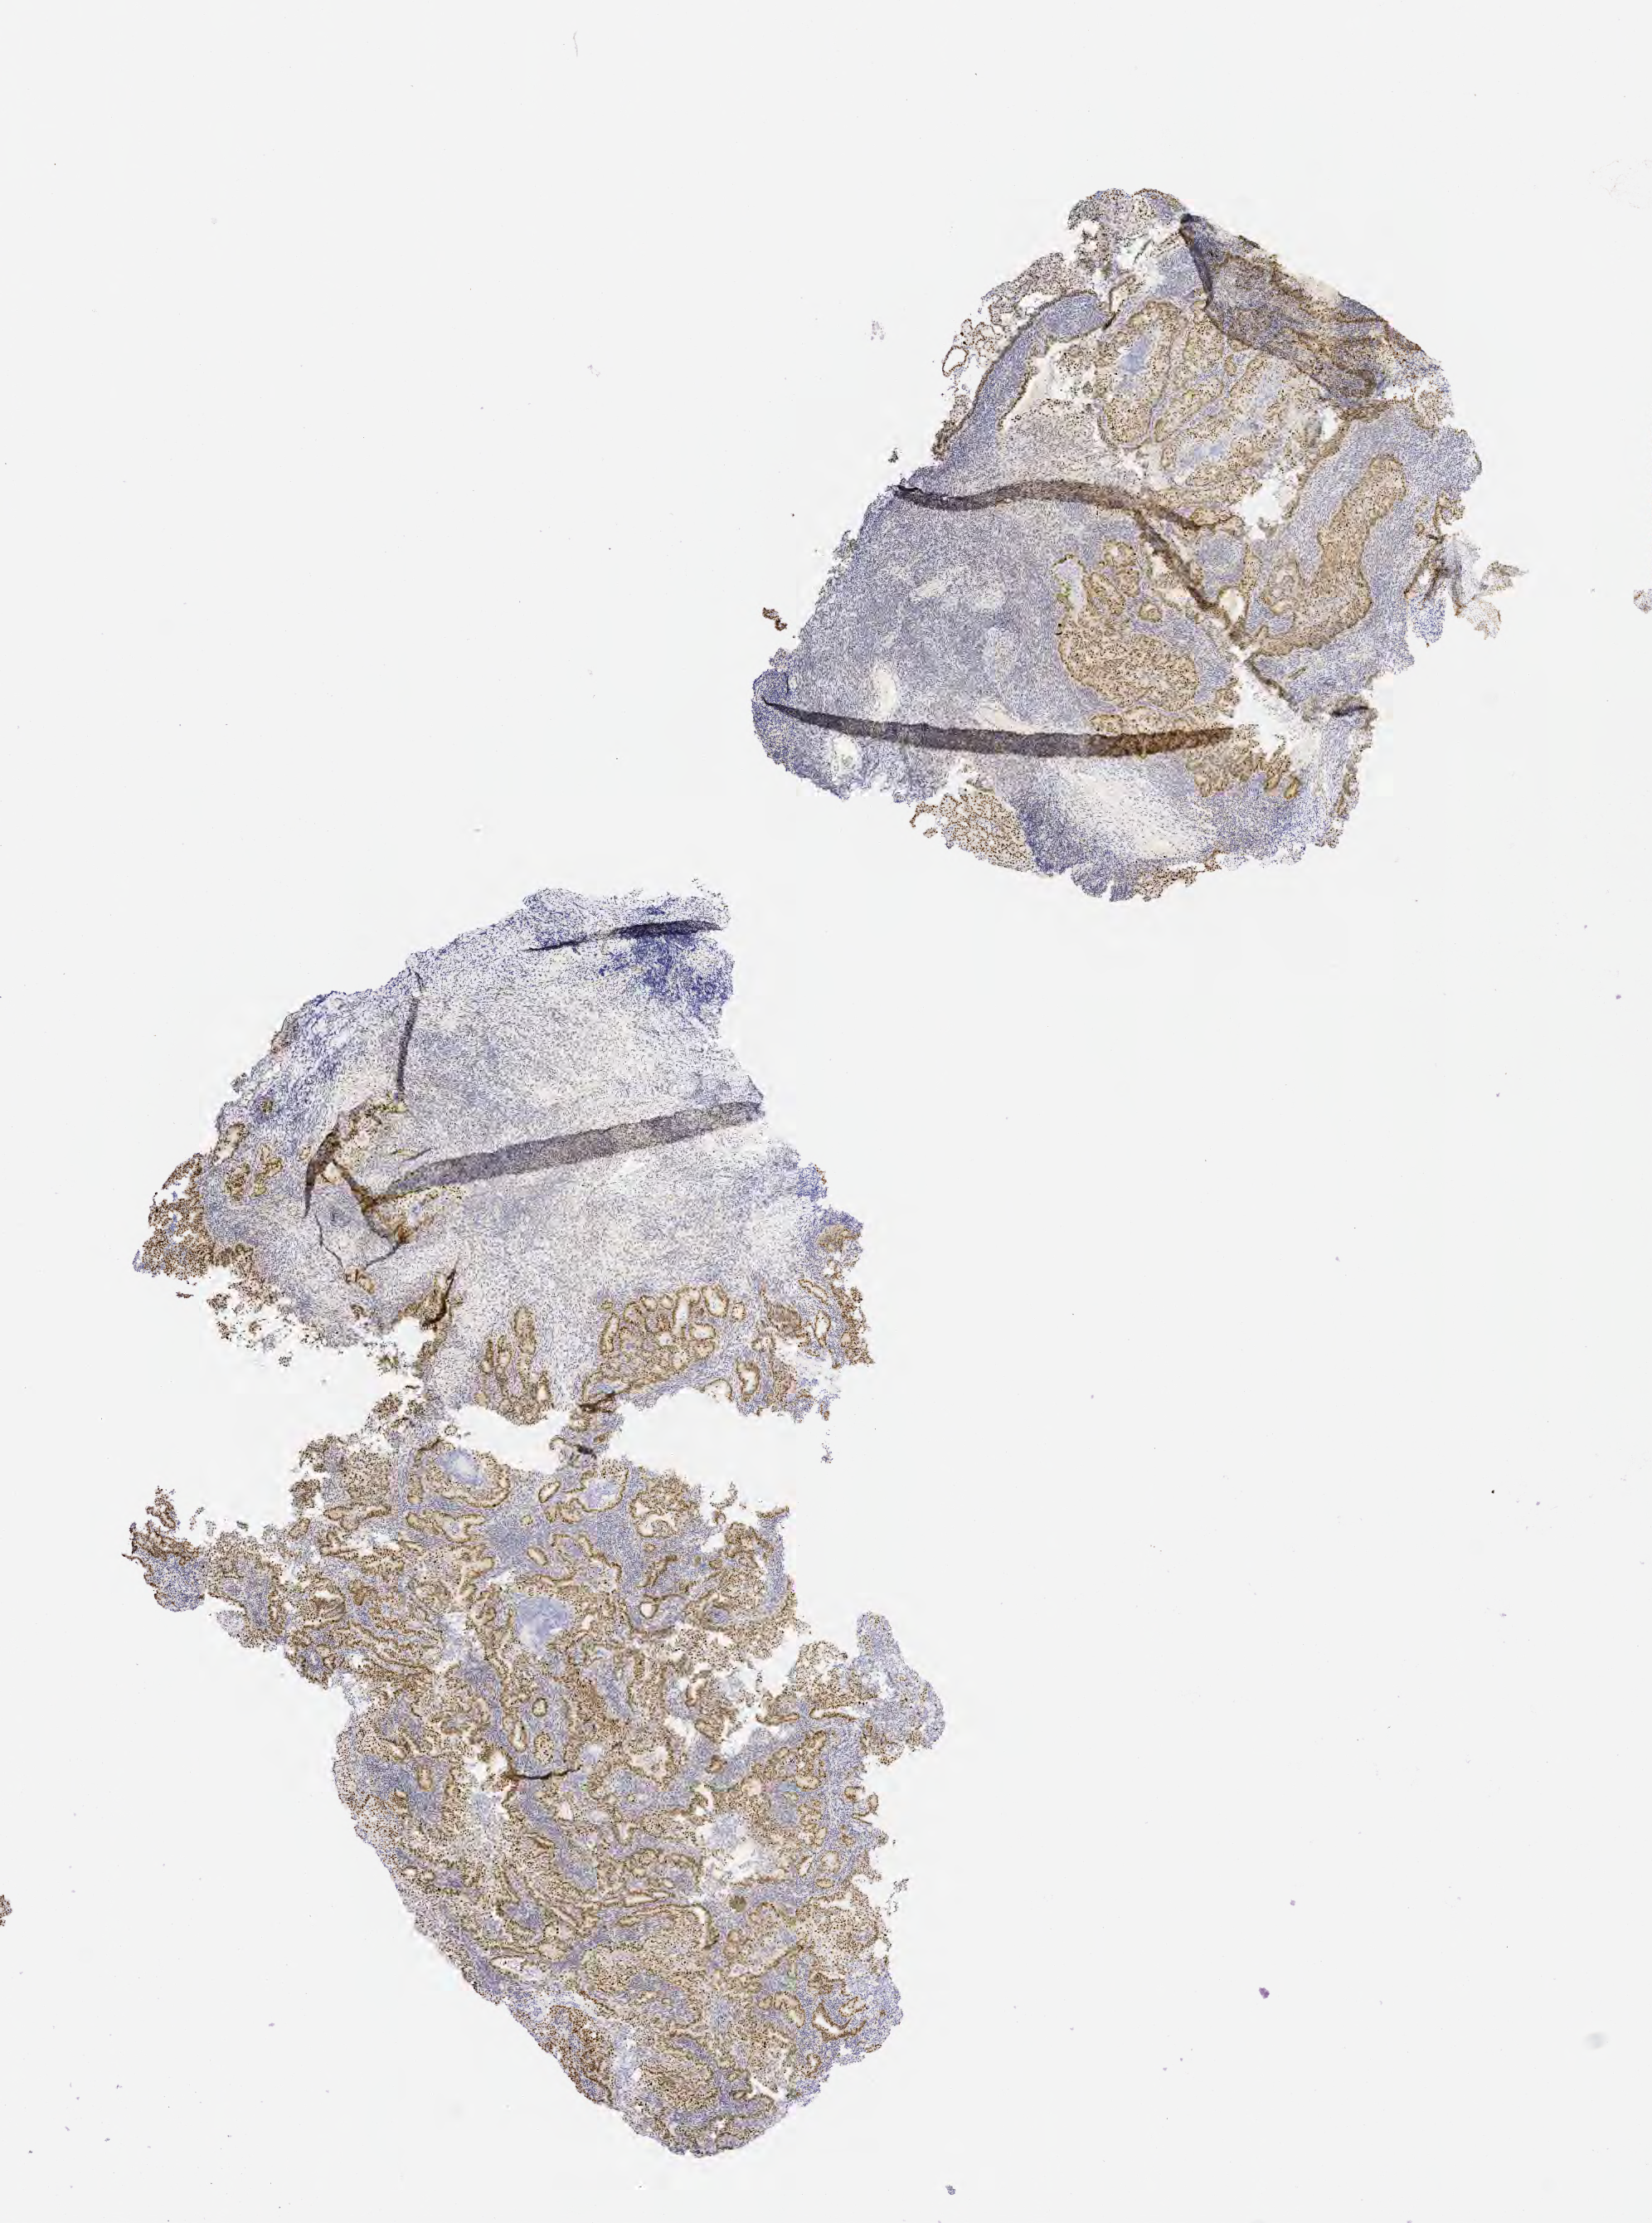
Immunohistochemistry (IHC) whole-slide image stained for p53 — whole scanned area (about 8.0 x 10.8 mm) shown as a low-resolution overview. Specimen: tumor tissue. Anatomic site: cervix. Patient female; aged 48.
- histologic diagnosis: Adenocarcinoma, NOS